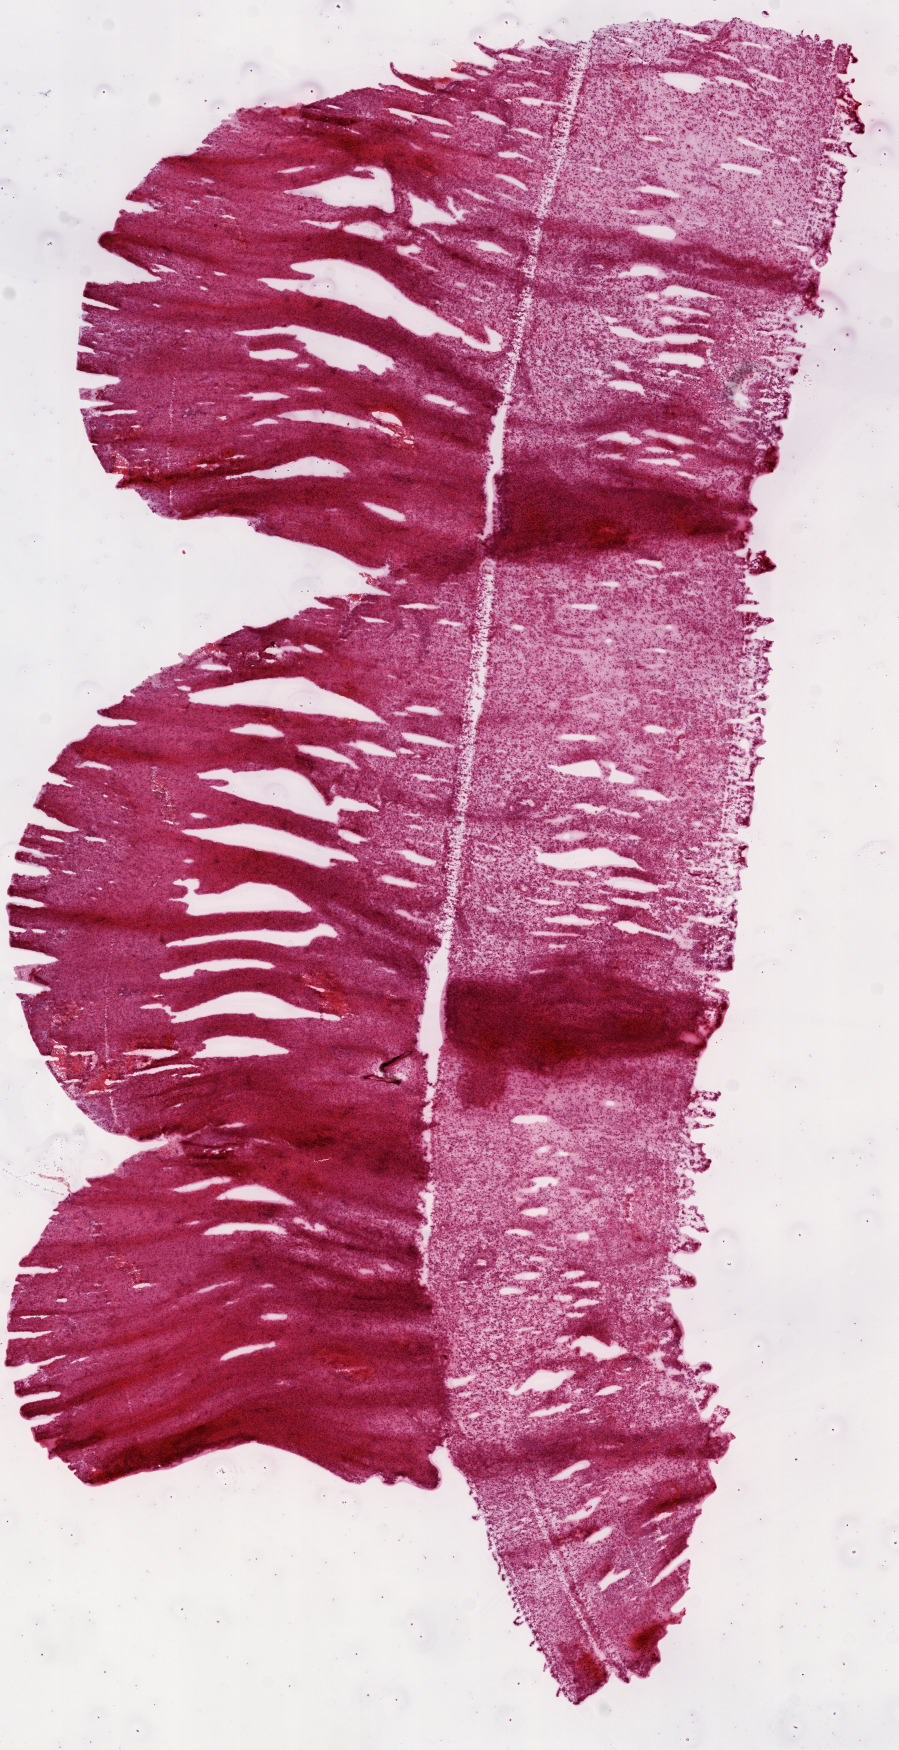
Digitized H&E-stained tissue section (whole slide), shown as a low-resolution overview of the whole scanned area (about 7.3 x 14.1 mm, acquisition: 20x scan); frozen section; brain, primary tumour sample. Female patient; age at initial diagnosis 70 years. Composition of this section per pathologist review: tumour cells 100%, tumour nuclei 80%, normal cells 0%, stromal cells 0%, necrosis 0%. Infiltration values recorded for this section: lymphocyte infiltration 0%, neutrophil infiltration 0%.
Histologic diagnosis: Glioblastoma.